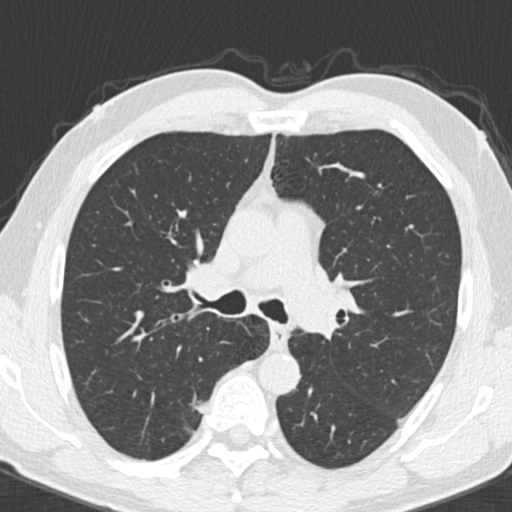
Low-dose screening chest CT, axial slice. Third annual screen. Lung window (W 1500 / L -600 HU). 2 mm slice thickness. Standard (soft-tissue) reconstruction kernel (B30f). Slice 66 of 192 in the series. 512 × 512 image matrix. Male, age 55 years at enrolment.
Expert-annotated lung lesion, box from (x=169, y=386) to (x=221, y=439) px. Reader record for this screening exam (exam-level; its link to the box is not recorded): non-calcified nodule or mass ≥4 mm, right upper lobe, 9 × 7 mm, smooth margins, soft tissue attenuation, pre-existing on the prior screen: no. Official screen result: positive, other. Lung cancer was diagnosed 221 days after this screen: adenocarcinoma, NOS, right upper lobe, poorly differentiated (G3), stage IA (AJCC 6th edition), 15 mm at pathology.